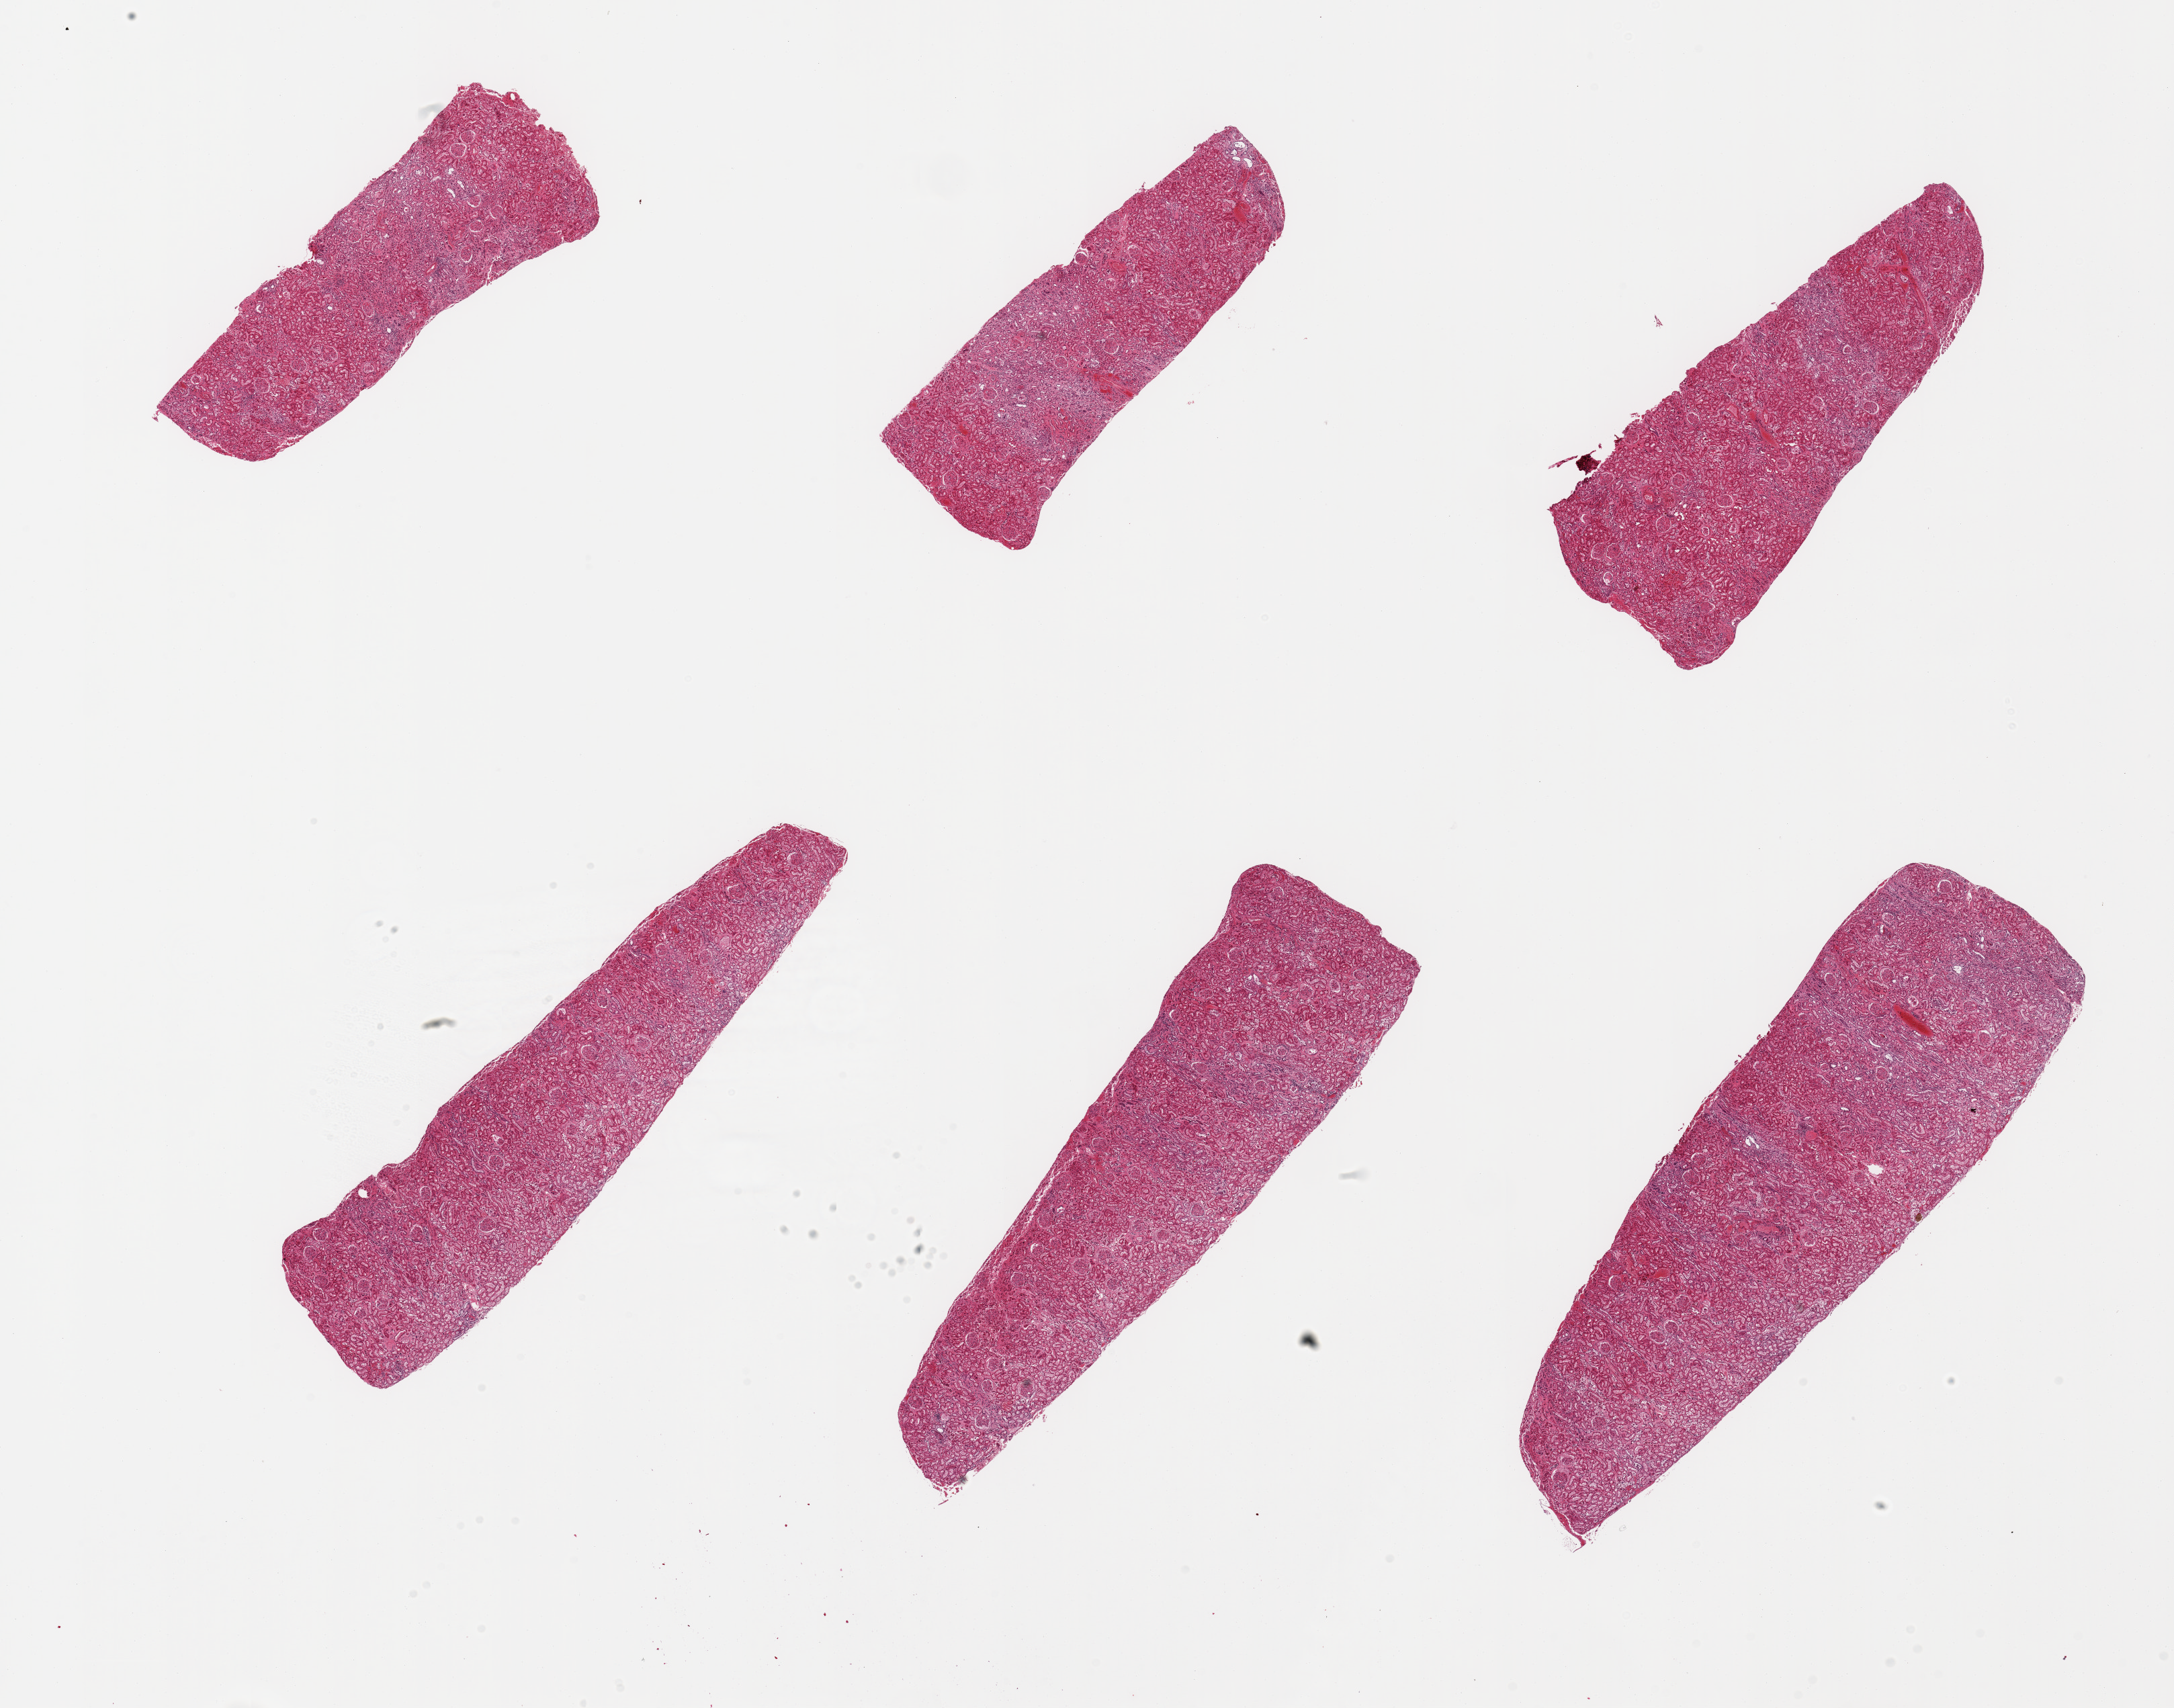
Digitized hematoxylin and eosin (H&E)-stained section — low-resolution overview of the scanned area, about 25.6 x 20.1 mm (slide scanned at 20x); PAXgene-fixed, paraffin-embedded tissue; target tissue: renal cortex; donor tissue sample. Donor sex: male.
Reviewer comment on this tissue sample: 6 pieces; tubules main site of autolysis; no sign of active or chronic disease.